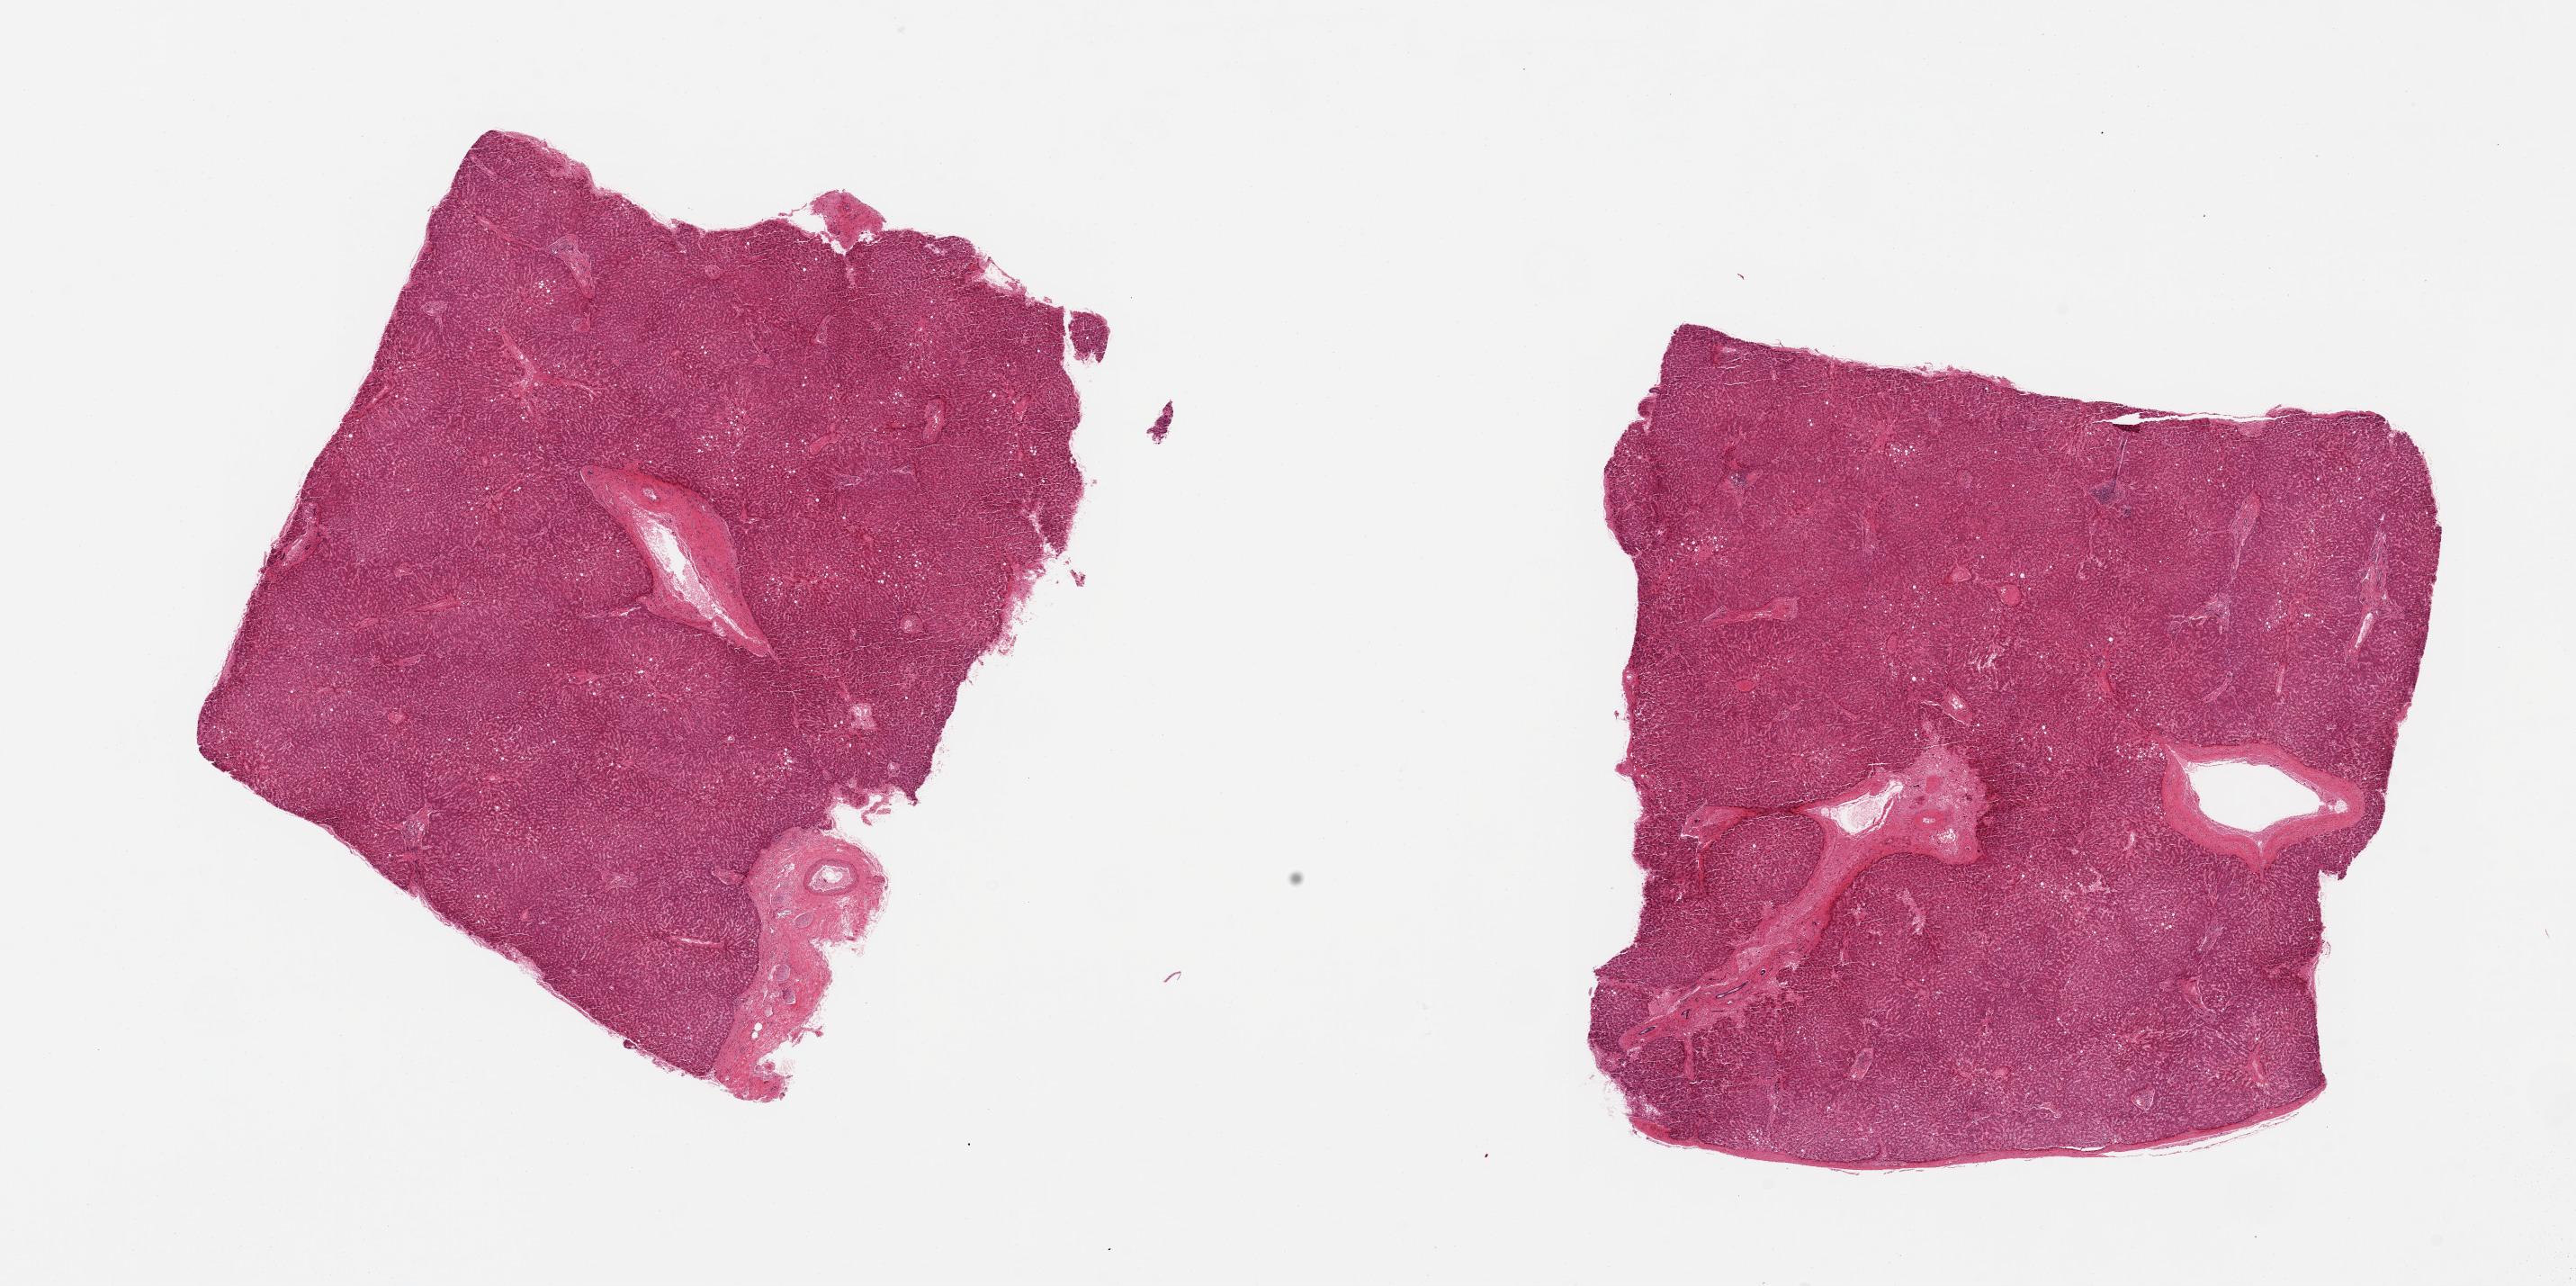
Digitized haematoxylin and eosin-stained section, low-resolution overview of the scanned area, about 22.6 x 11.3 mm (from a 20x scan), PAXgene-fixed paraffin-embedded (PFPE) section, section of liver (target tissue), tissue donor sample. Female donor.
Reviewer comment on this tissue sample: 2 pieces. 8x7 & 7x7mm; <5% macrovesicular steatosis.